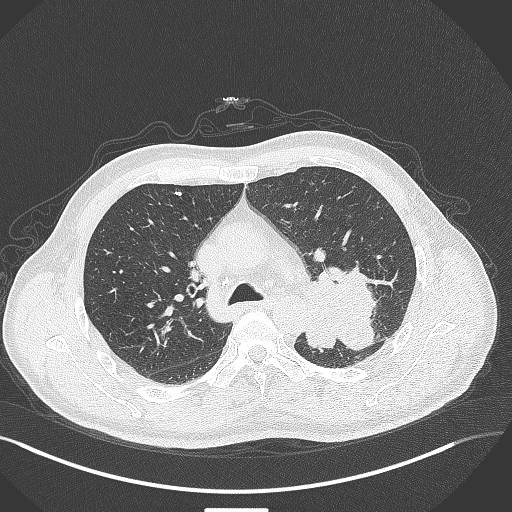
Chest CT, one axial slice; slice 284 of 429 in the series (ordered by position); 120 kVp; lung window (W 1500 / L -600 HU); 1 mm slice thickness; 512 × 512 image matrix, field of view 400 × 400 mm. Male patient, age 55 years. Case-level facts recorded for this patient, not image findings: clinical TNM (as recorded): T3 N0 M1c; histopathological grade: G3.
Structures marked on this image (bounding box drawn by a radiologist):
- lung tumour (recorded histology: adenocarcinoma): bounding box (x1, y1, x2, y2) in pixels: (302, 262, 385, 353)